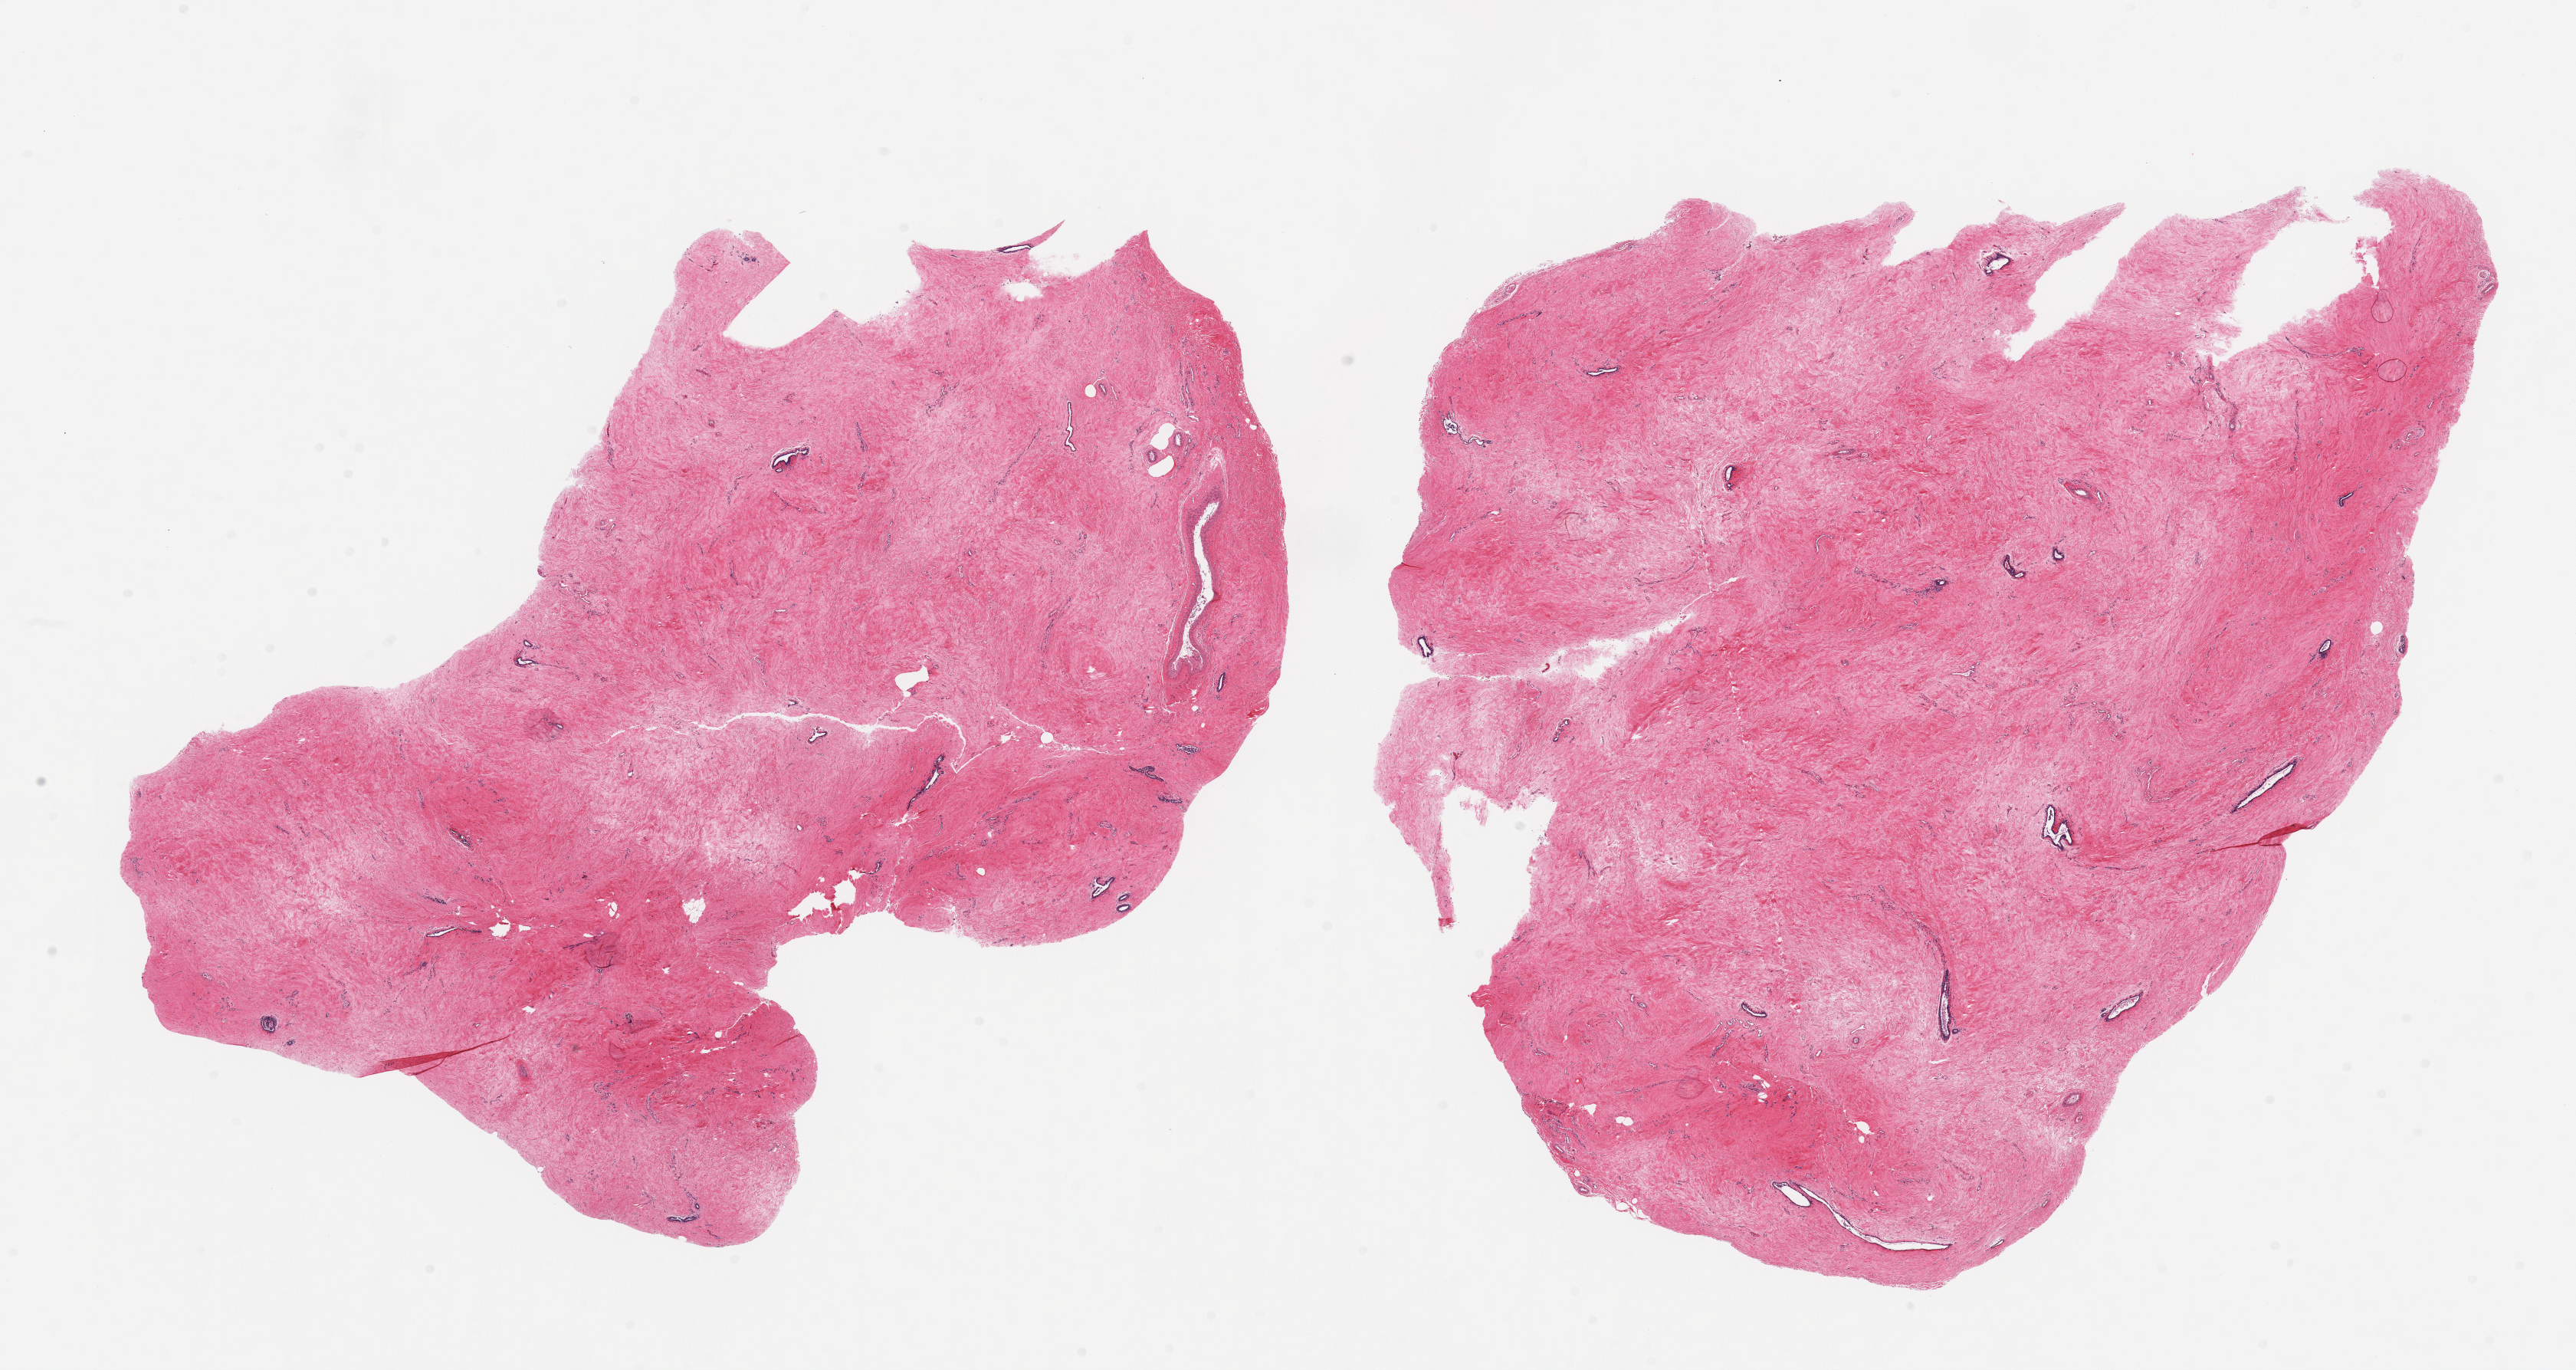
Hematoxylin and eosin (H&E) whole-slide image — low-resolution overview of the scanned area, about 26.6 x 14.1 mm, PAXgene-fixed, paraffin-embedded tissue, sampled site (target tissue): breast, donor tissue sample. Donor: male.
Pathologist's review note for this sample: 2 pieces; dense fibrous stroma with embedded small ductal structures.